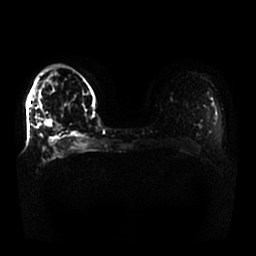
Breast MRI, one axial slice; slice 10 of 25 in the series (ordered by position); diffusion-weighted series; image 2 of 4 stored at this slice position (different b-values; order by instance number); 1.5 T; 4 mm slice thickness; 256 × 256 image matrix. Female patient.
Outlined on this slice (manually delineated by an expert):
- tumour on diffusion-weighted imaging: bounding box <43,119,52,128> (left, top, right, bottom; pixels)